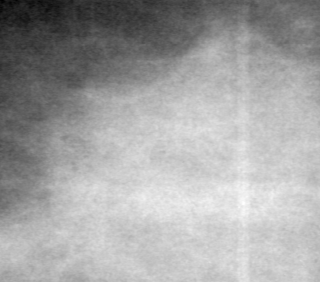
Region of interest cut from a scanned film mammogram (one marked finding), left breast, MLO view.
Marked abnormality: mass, shape lobulated, margins ill defined; BI-RADS assessment category 4; pathology (as recorded): malignant.